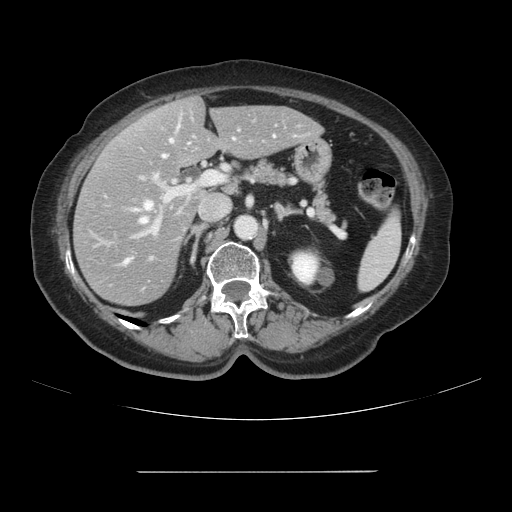
Contrast-enhanced abdominal CT, one axial slice. Position 54 of 111 along the scan axis. Intravenous contrast given. Soft-tissue window (W 400 / L 40 HU). 512 × 512 image matrix, field of view 400 × 400 mm. Female patient, age 74 years. From the clinical record (not read from this slice): diagnosis: colorectal cancer liver metastases, imaged before liver resection; multiple liver metastases: yes; largest metastasis: 1.1 cm.
Structures marked on this image (manually delineated by an expert):
- hepatic veins: bounding box (x1, y1, x2, y2) in pixels: (125, 140, 173, 263)
- liver: (74, 98, 320, 305)
- planned liver remnant (the part of the liver to remain after resection): (144, 98, 320, 167)
- portal vein (with intrahepatic branches): (132, 120, 301, 238)